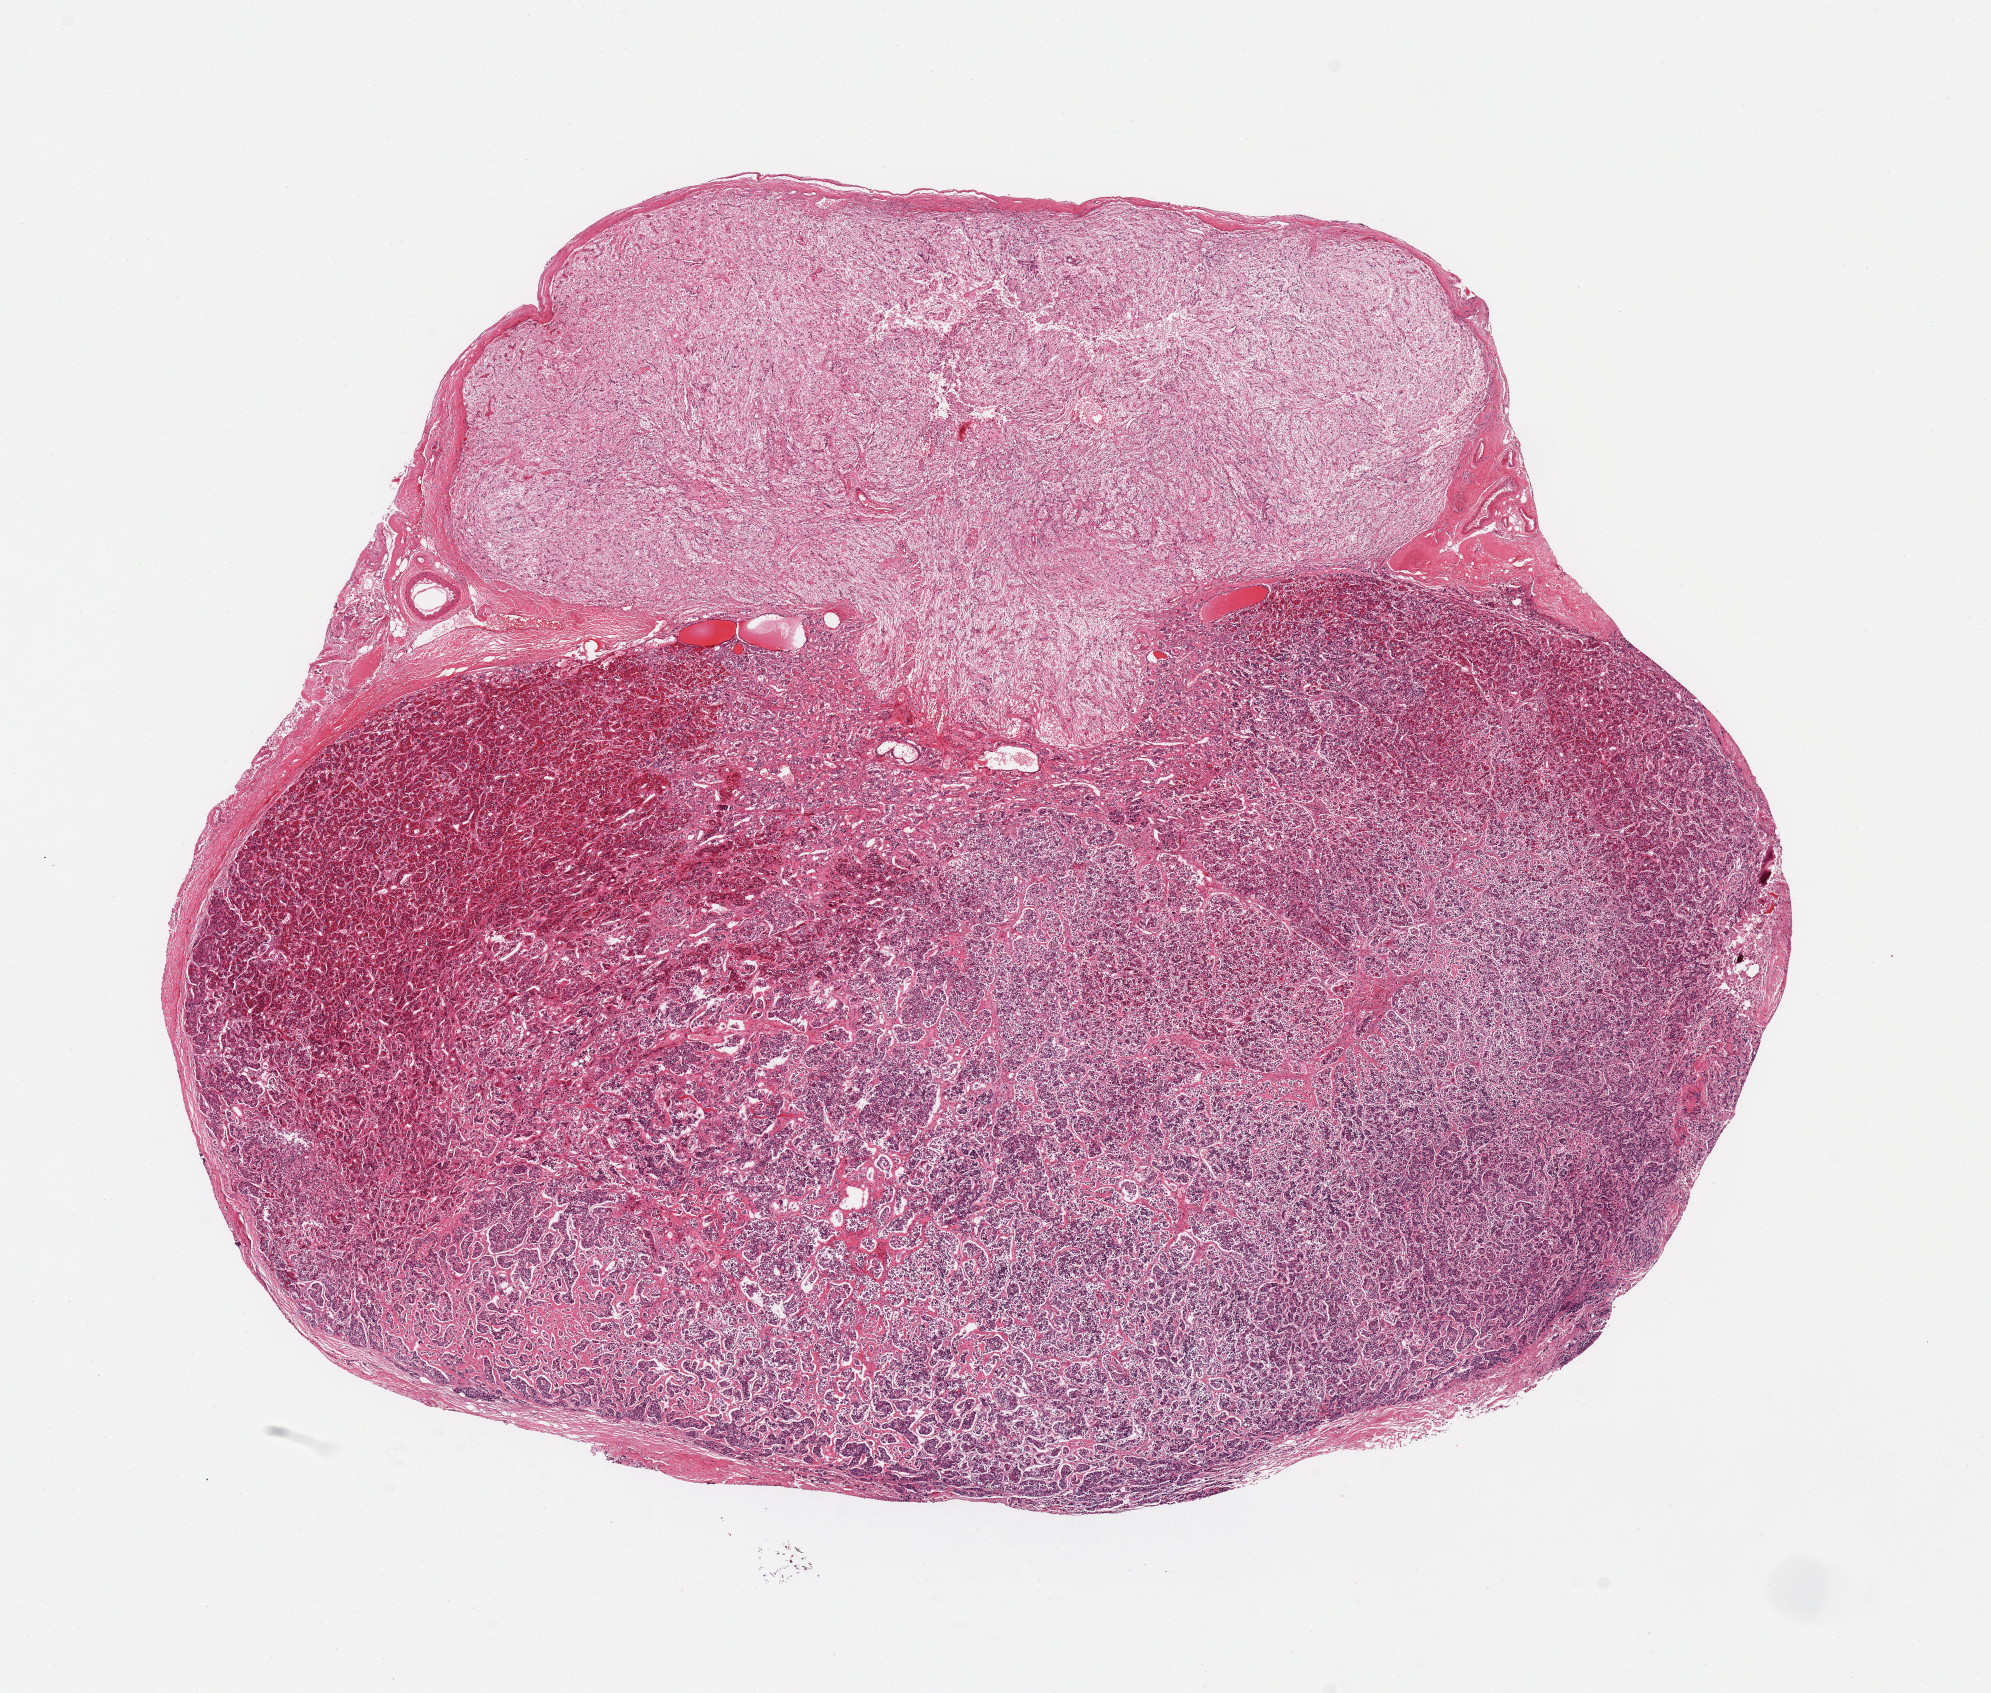
Whole-slide image, haematoxylin and eosin stain, brightfield, a low-resolution overview of the entire scanned area, about 15.8 x 13.4 mm. PAXgene-fixed paraffin-embedded (PFPE) section. Section of pituitary (target tissue). Tissue donor sample. Donor: male.
Review note (as recorded): 1 piece; ~70% adenohypophysis, 30% neurohypophysis, ~7x4mm.